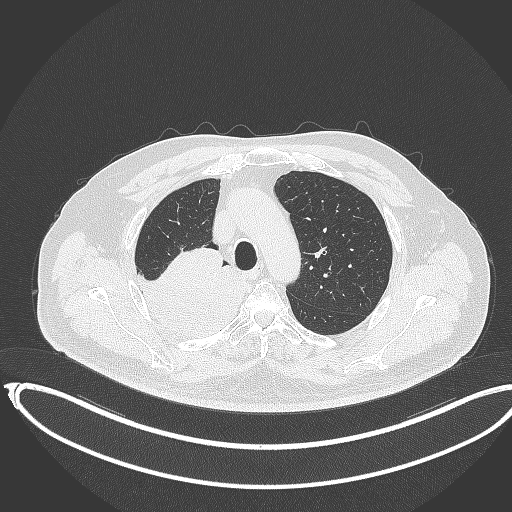
Chest CT, one axial slice; slice 273 of 403 in the series (ordered by position); reconstruction kernel B70f; 120 kVp; lung window (W 1500 / L -600 HU); 1 mm slice thickness; 512 × 512 image matrix, field of view 436 × 436 mm. Male patient, age 68 years. Case-level facts recorded for this patient, not image findings: clinical TNM (as recorded): T2a N0 M0.
Outlined on this slice (bounding box drawn by a radiologist):
- lung tumour (recorded histology: adenocarcinoma): bounding box (x1, y1, x2, y2) in pixels: (134, 244, 244, 343)